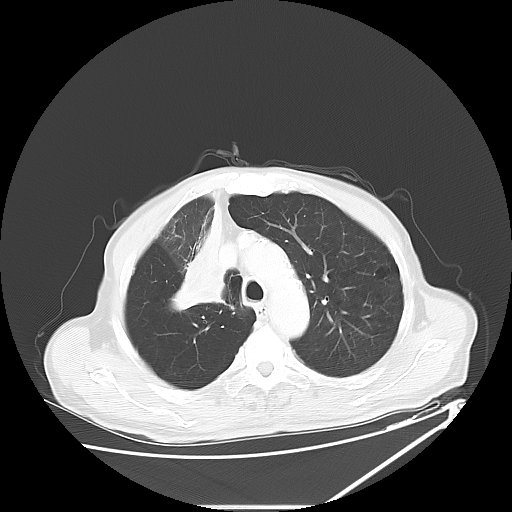
Chest CT, one axial slice; reconstruction kernel LUNG; lung window (W 1500 / L -600 HU); 5 mm slice thickness; 512 × 512 image matrix, field of view 410 × 410 mm. Patient: male, 73 years. From the clinical record (not read from this slice): clinical TNM (as recorded): T2a N1 M0.
Structures marked on this image (bounding box drawn by a radiologist):
- lung tumour (recorded histology: squamous cell carcinoma): bounding box (x1, y1, x2, y2) in pixels: (172, 195, 232, 324)